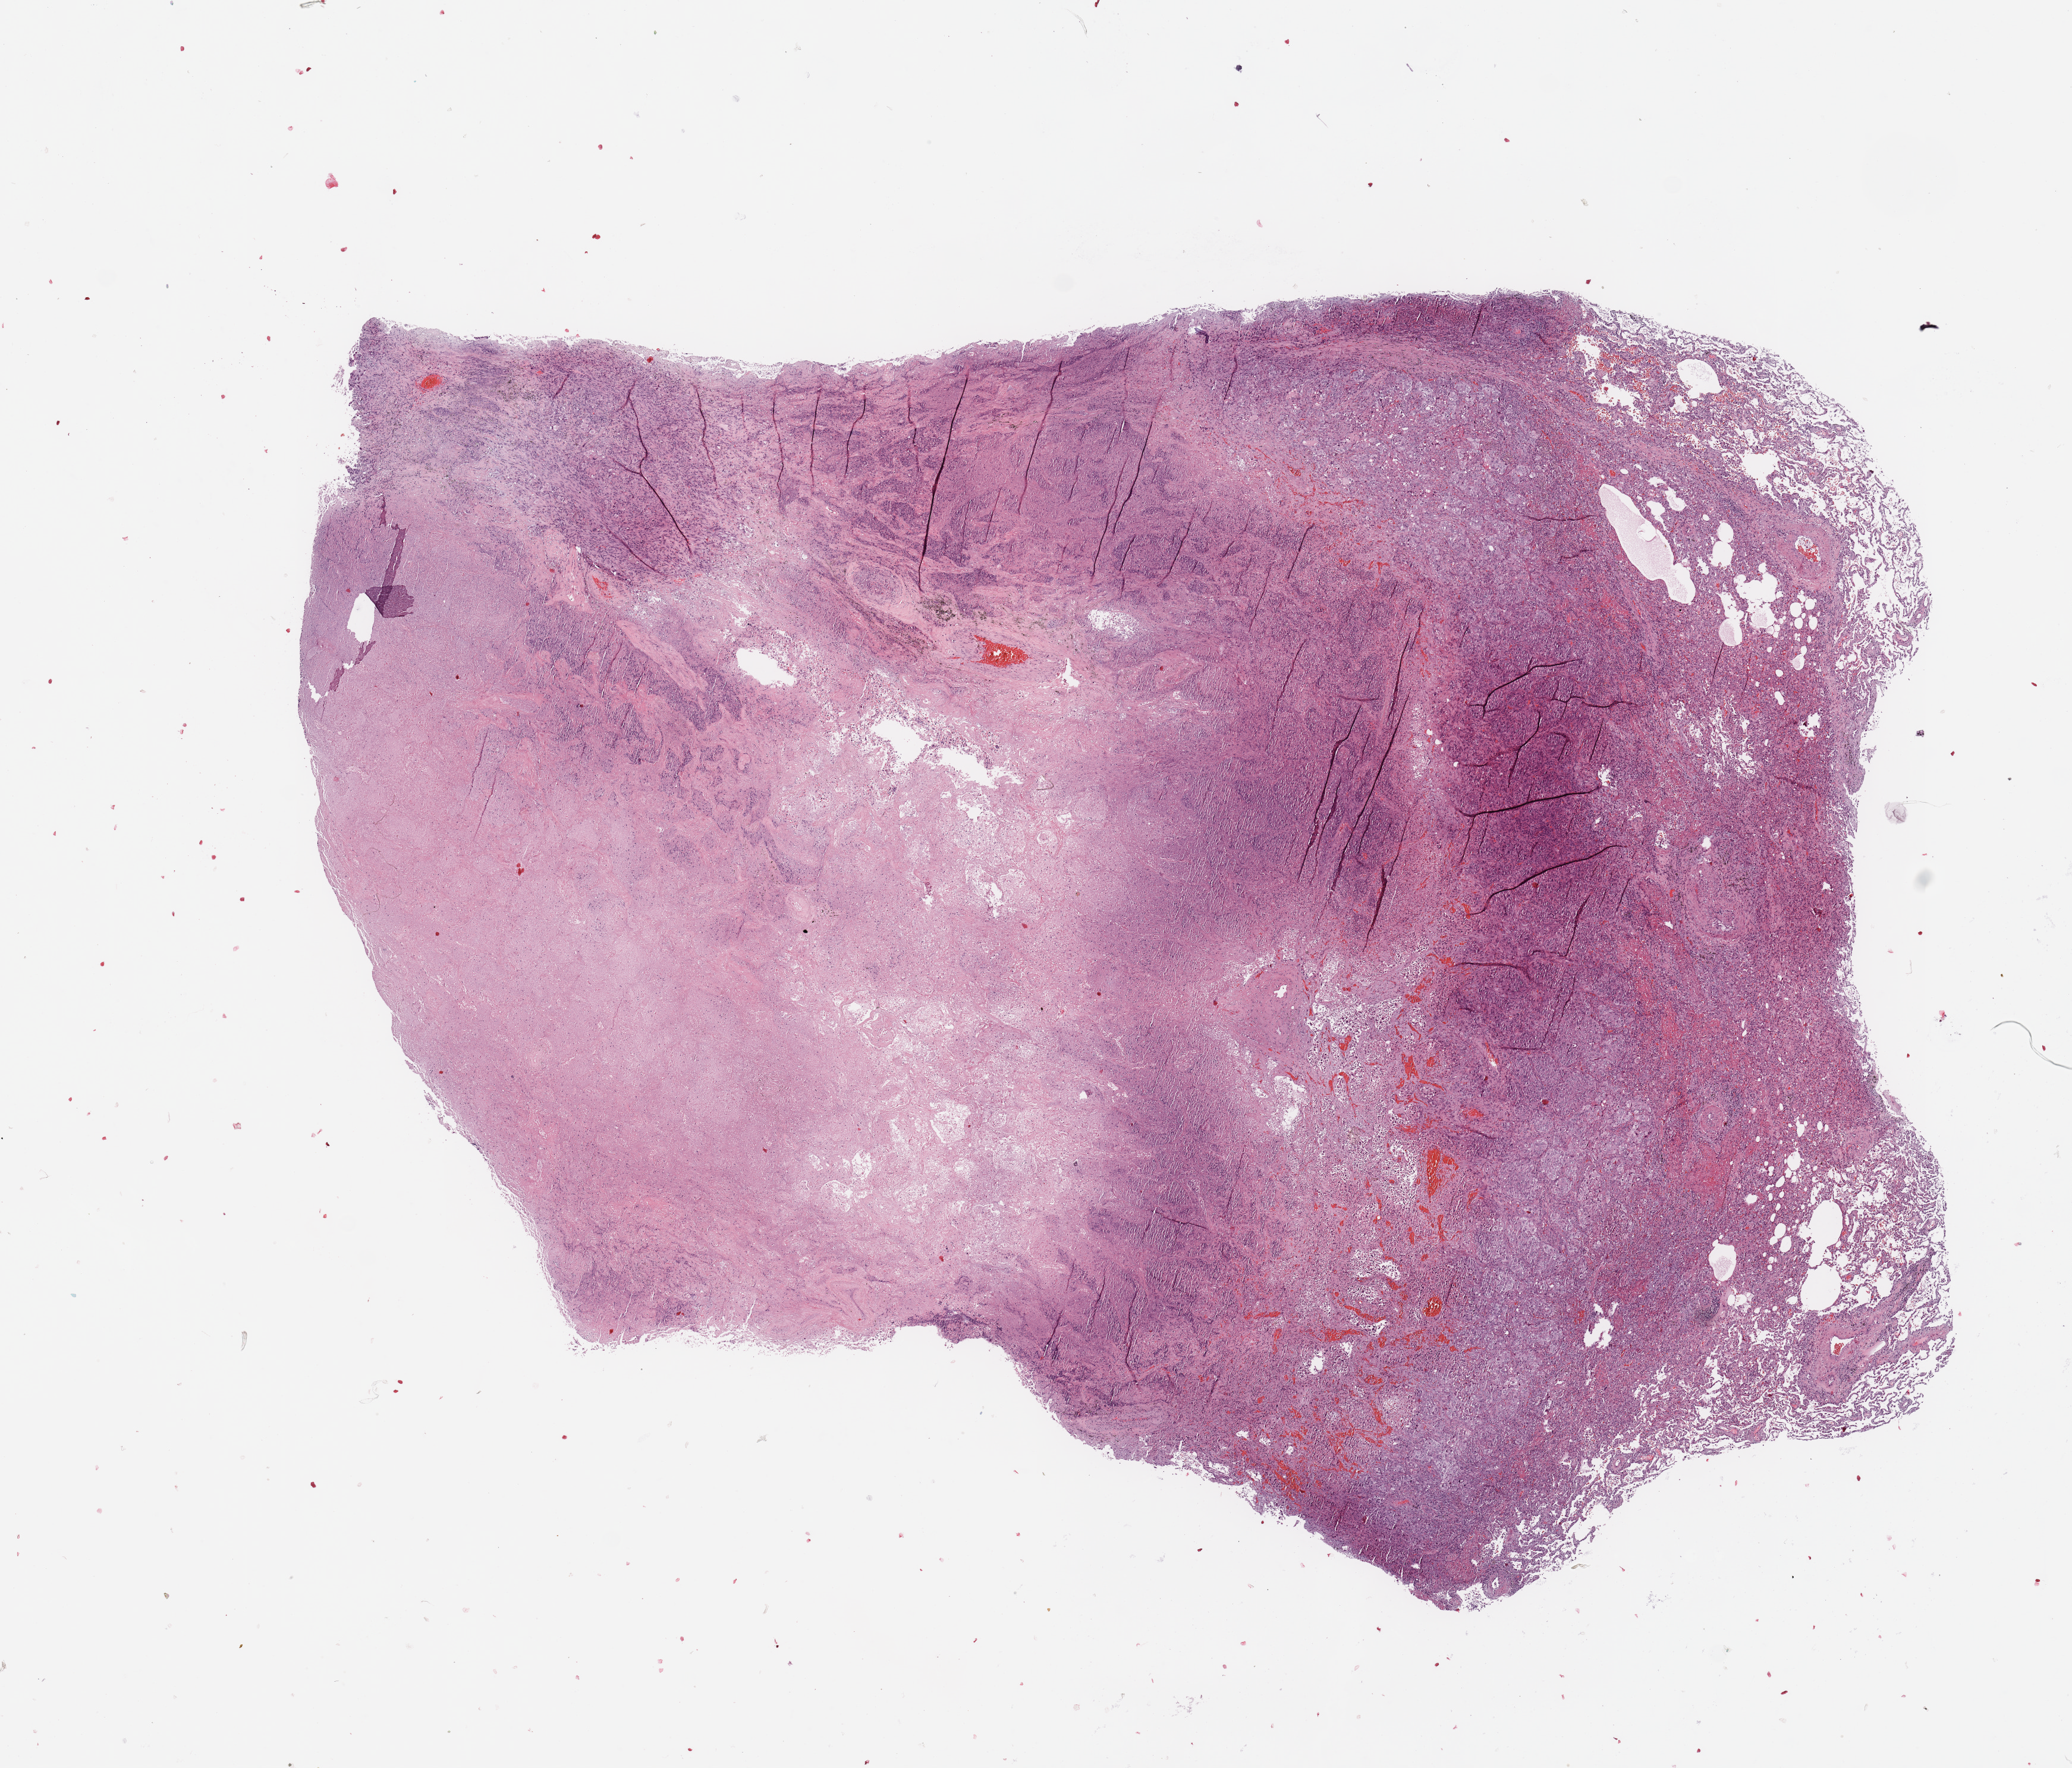
Whole-slide histology image, H&E — low-resolution overview of the scanned area, about 13.8 x 11.8 mm, lung, tumour tissue. Male, 65 y/o. Histologic grade: G3 (poorly differentiated).
AJCC pathologic stage: IIIA. Histologic diagnosis: Adenocarcinoma, NOS.